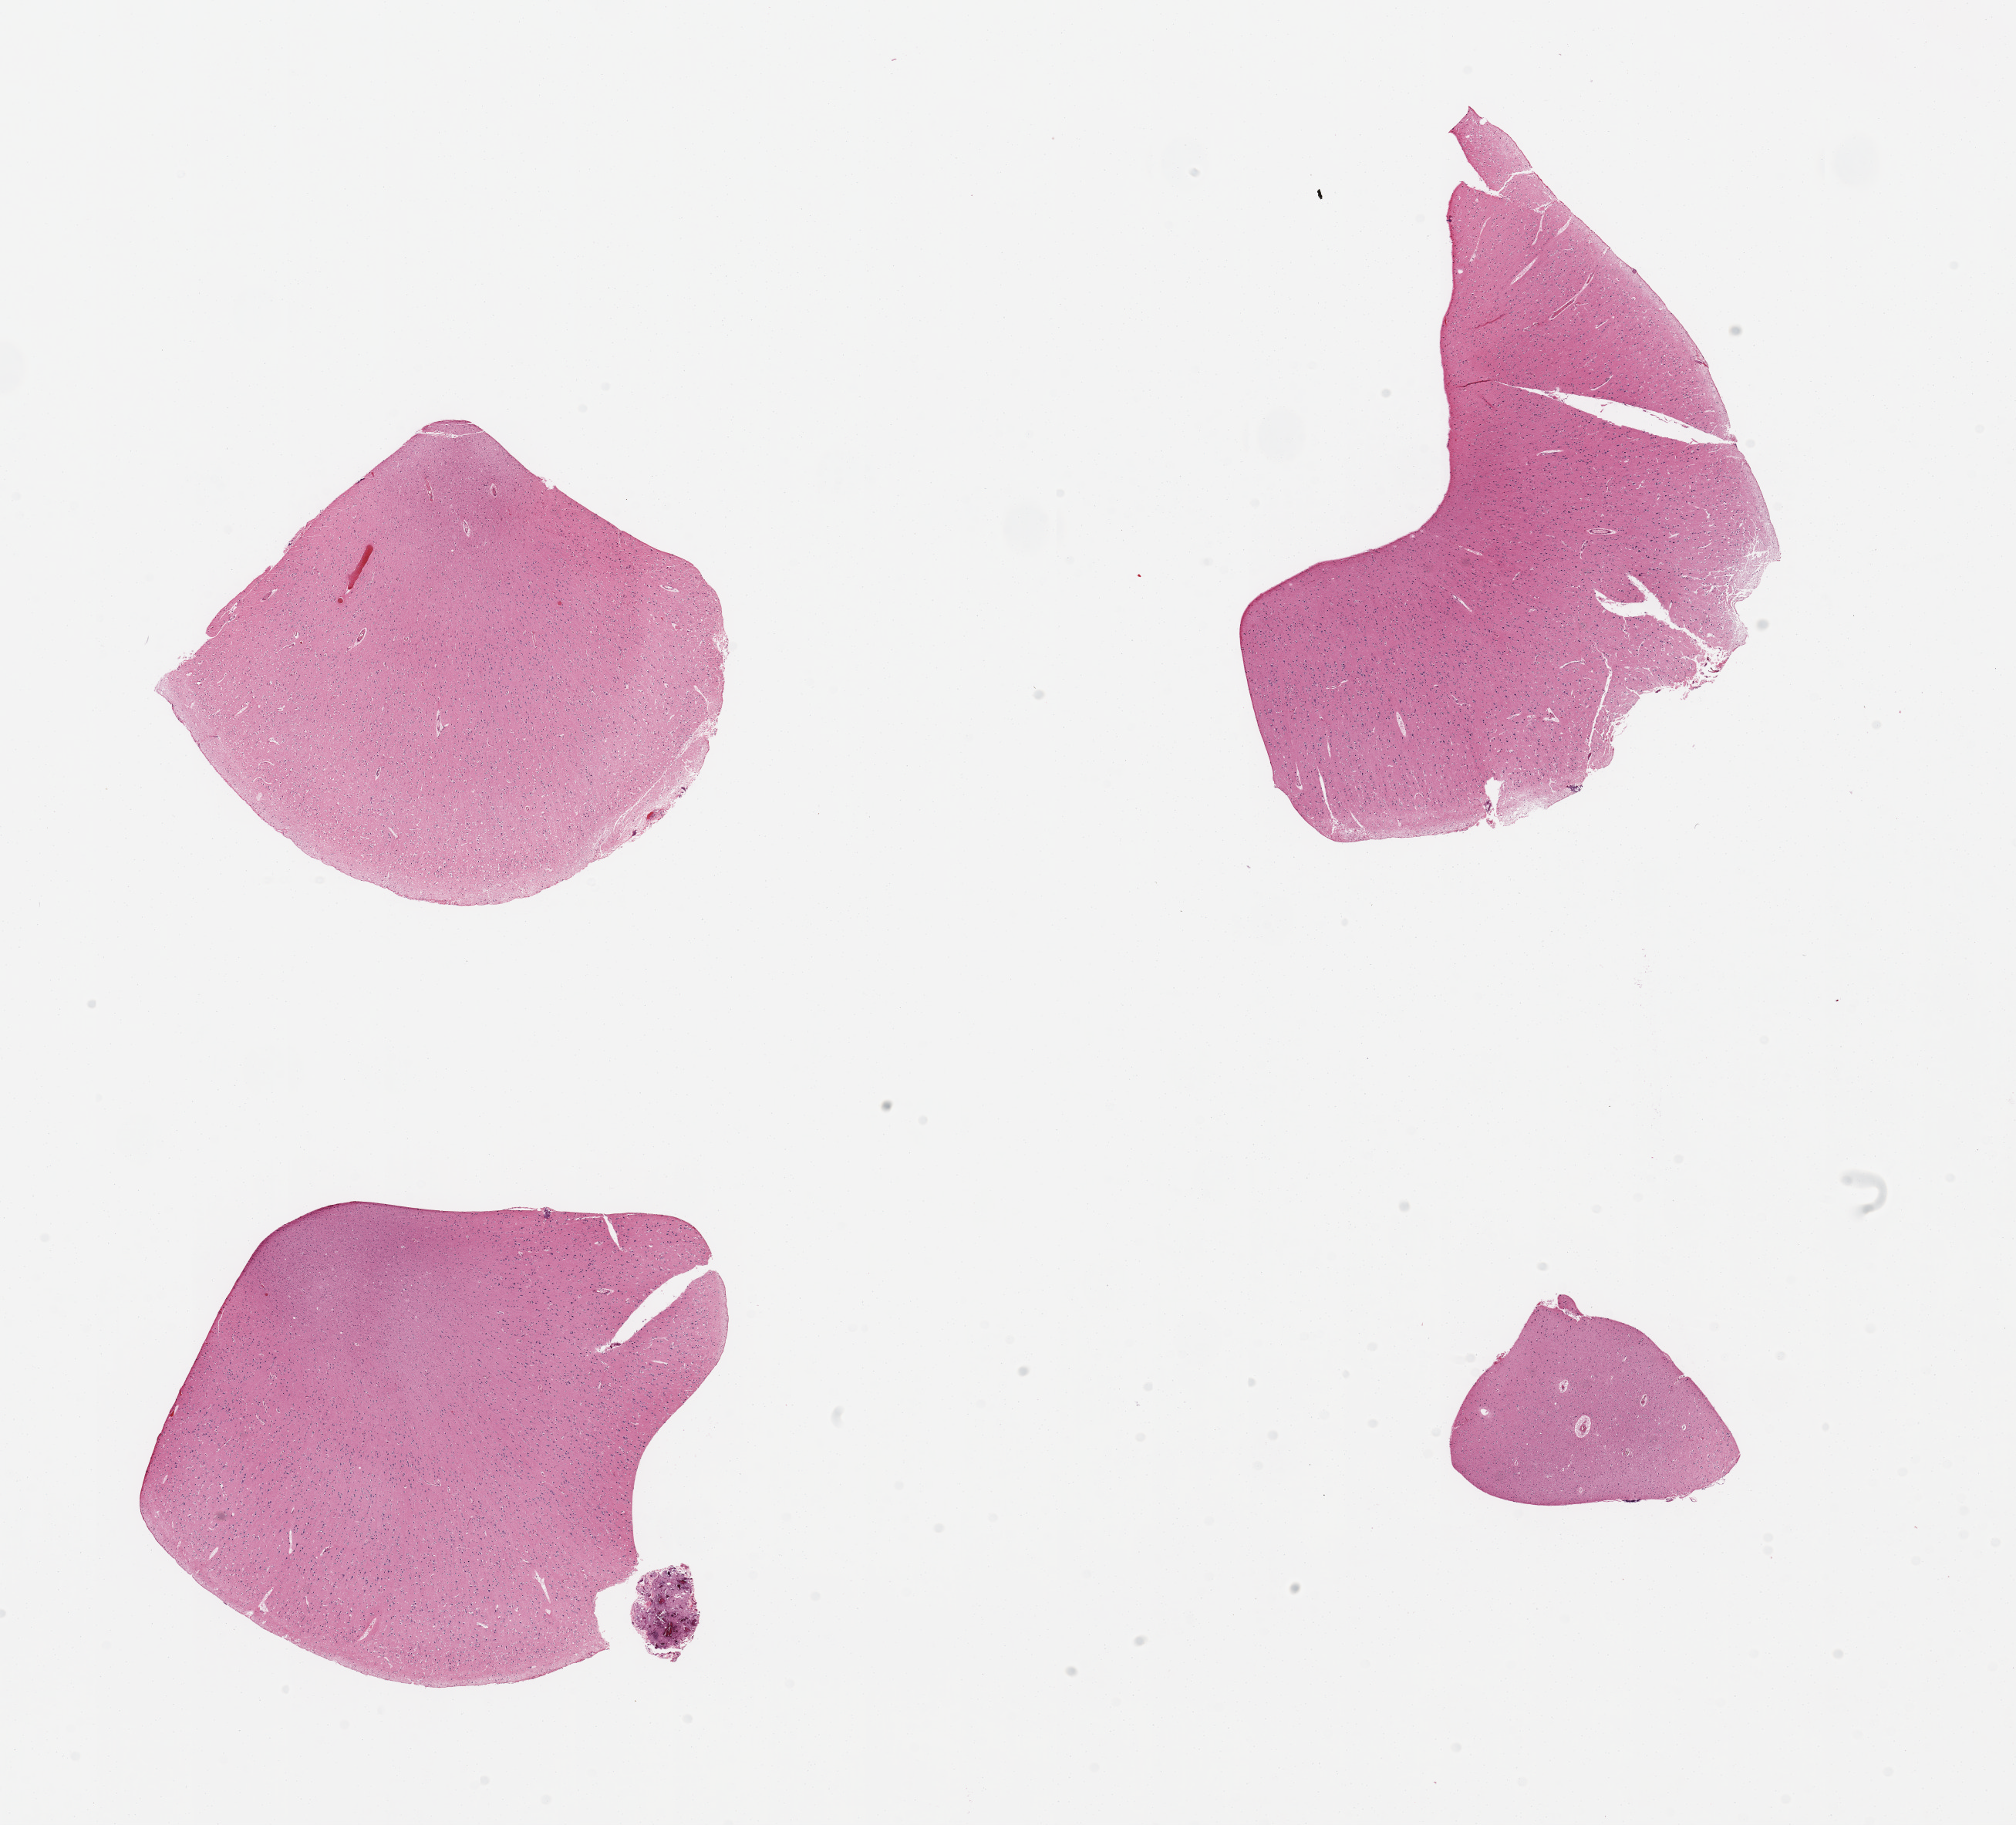
Digitized H&E-stained section — low-resolution overview of the scanned area, about 20.7 x 18.7 mm, PAXgene-fixed paraffin-embedded (PFPE) section, target tissue: cerebral cortex, donor tissue sample. Donor sex: male.
Review note (as recorded): 4 pieces; 1mm external focus of debris, possible bone and tissue.